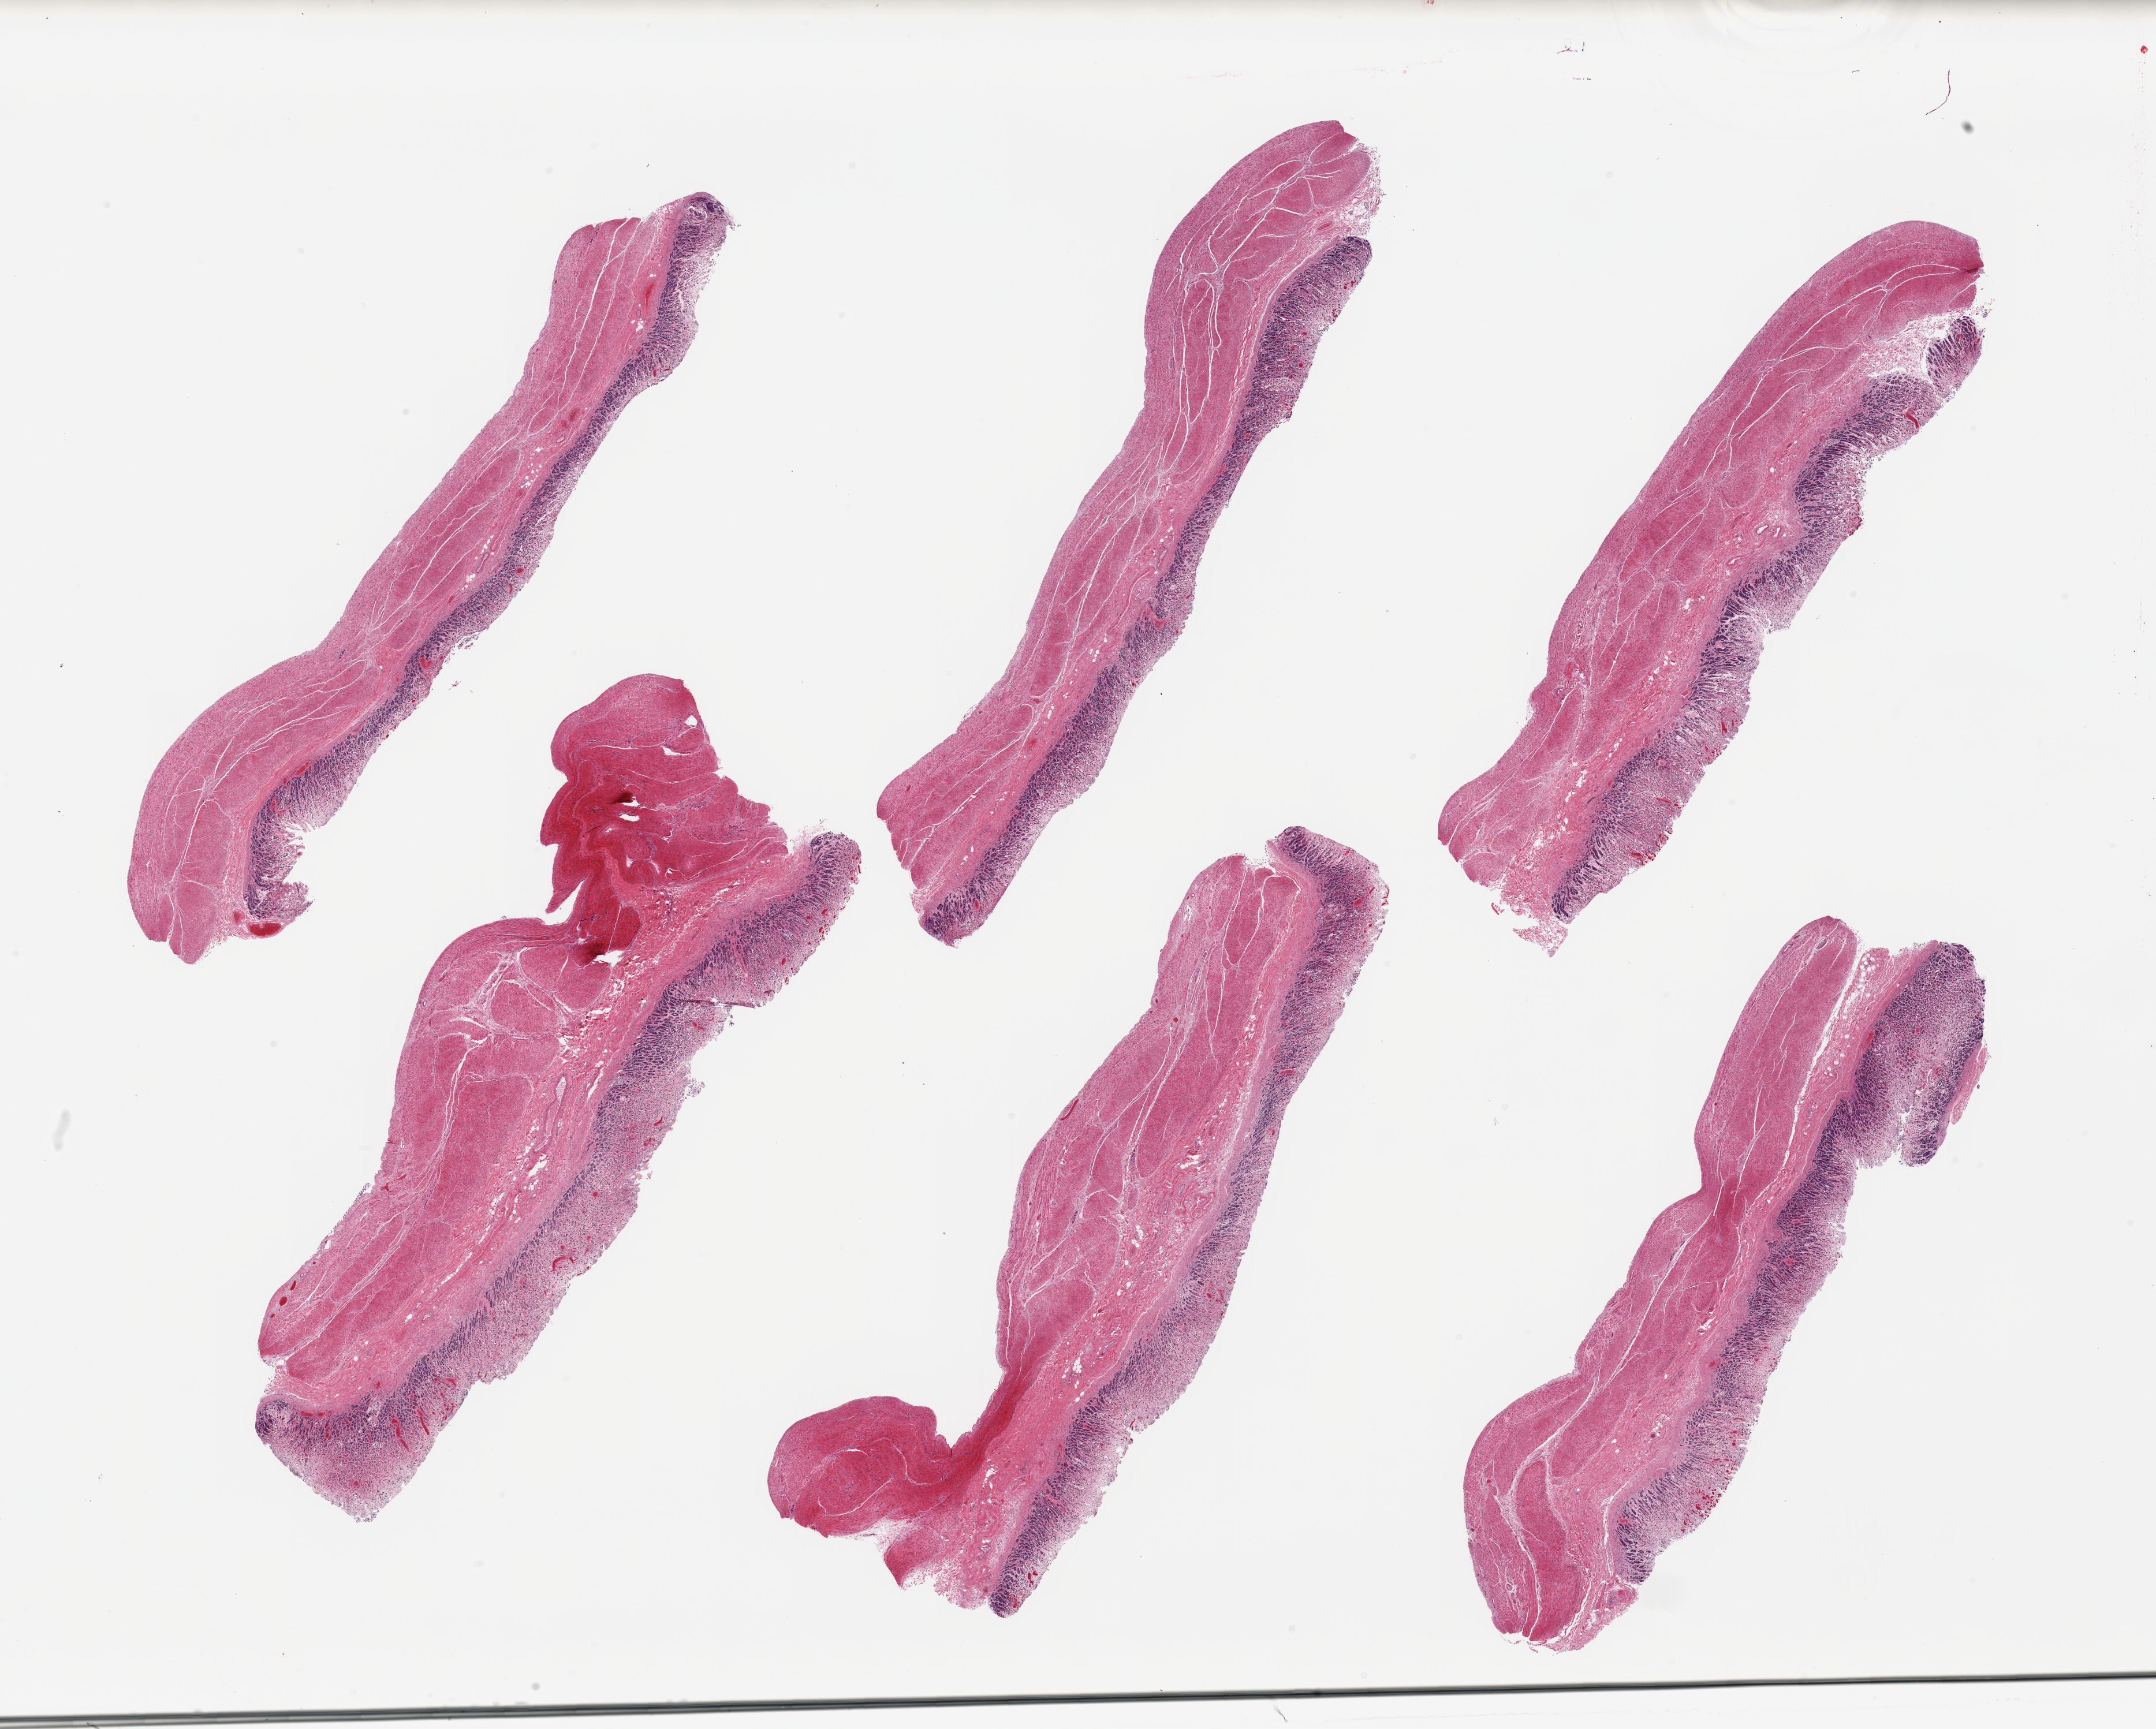
H&E whole-slide image — low-resolution overview of the scanned area, about 29.5 x 23.7 mm; PAXgene-fixed, paraffin-embedded tissue; sampled site (target tissue): stomach; tissue donor sample. Male donor.
* review note (as recorded): 6 pieces; moderate to severe mucosal autolysis and congestion; preserved muscularis